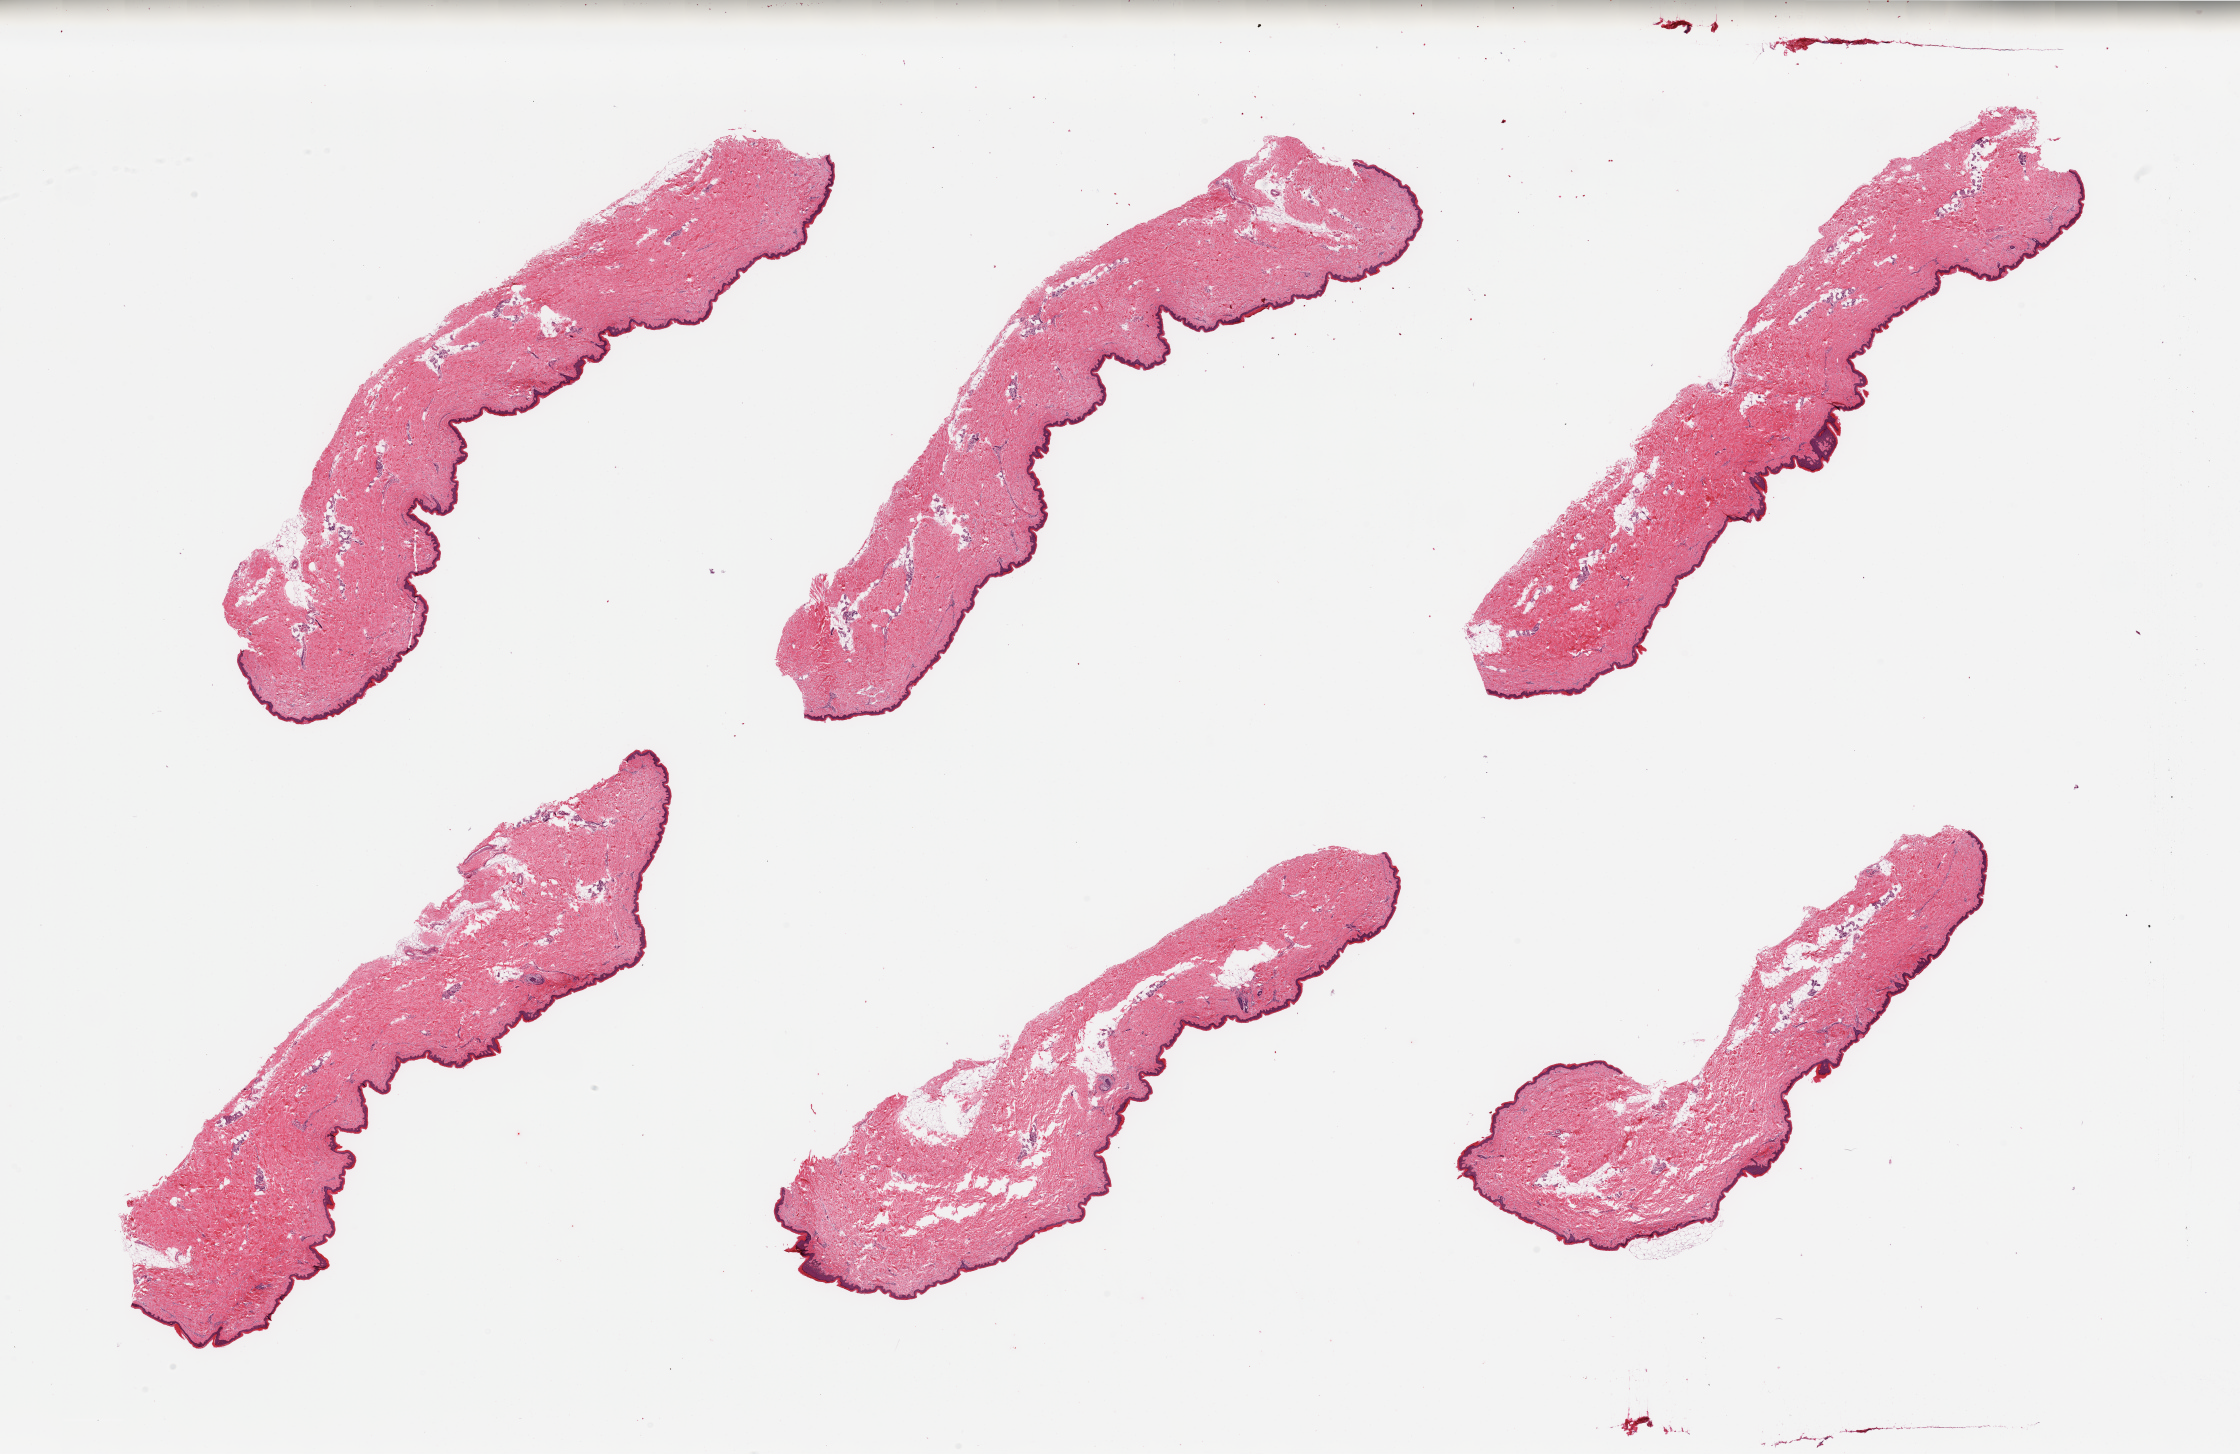
Whole-slide image, haematoxylin and eosin stain, shown as a low-resolution overview of the whole scanned area (about 35.4 x 23.0 mm, acquisition: 20x scan). PAXgene-fixed paraffin-embedded (PFPE) section. Sampled site (target tissue): skin of lower leg. Tissue donor sample. Donor sex: female.
Pathologist's review note for this sample: 6 pieces; 5-10% dermal fat; well trimmed.